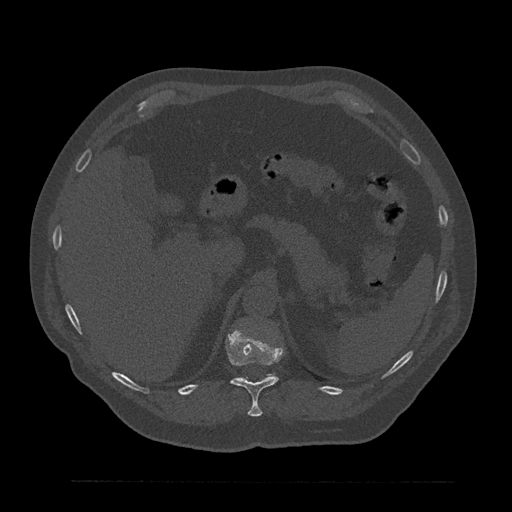
CT including the spine, one axial slice. Position 278 of 797 along the scan axis. Bone window (W 1800 / L 400 HU). 0.5 mm slice thickness. 512 × 512 image matrix. Patient: male, 61 years. Case-level facts recorded for this patient, not image findings: primary cancer: prostate.
Annotated regions visible in this slice (semi-automatic segmentation, software-assisted and operator-edited):
- T11 vertebra: box from (x=226, y=329) to (x=284, y=417) px